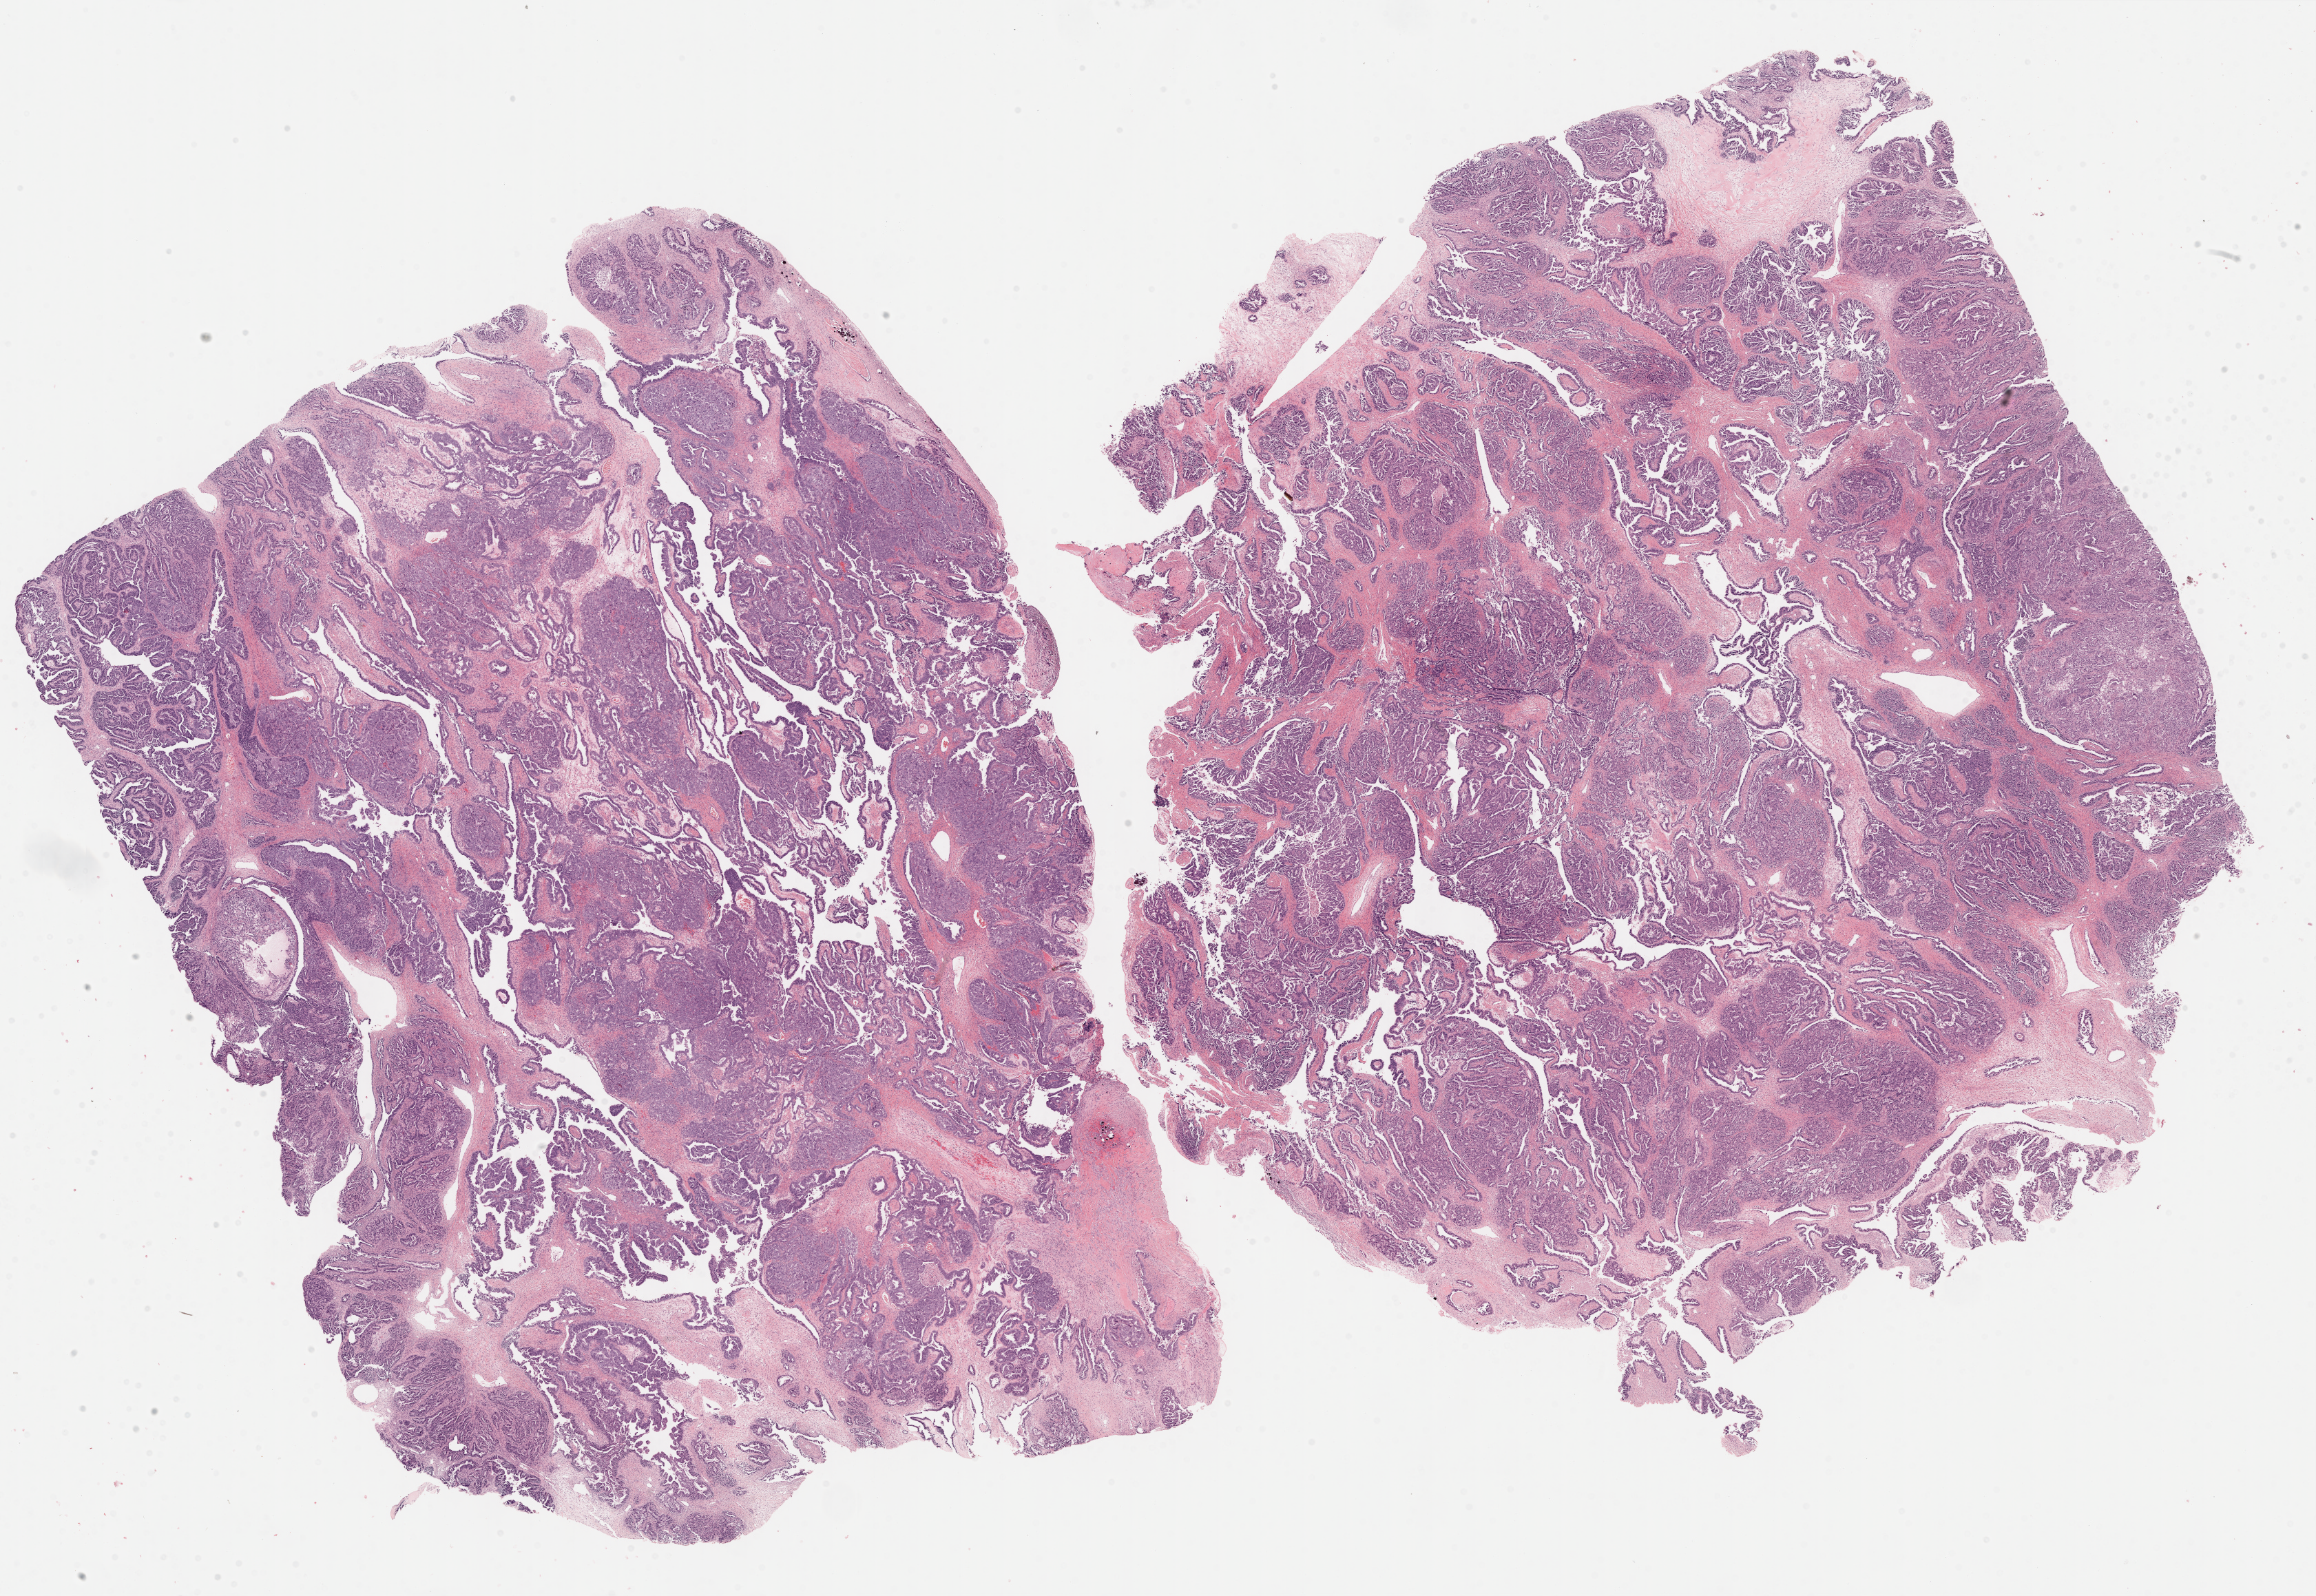
Hematoxylin and eosin (H&E) stained whole-slide image — whole scanned area (about 27.2 x 18.7 mm) shown as a low-resolution overview, formalin-fixed paraffin-embedded (FFPE) diagnostic section, primary tumour sample from the ovary. Female patient; age at initial diagnosis 76 years.
Diagnosis: Serous cystadenocarcinoma, NOS.